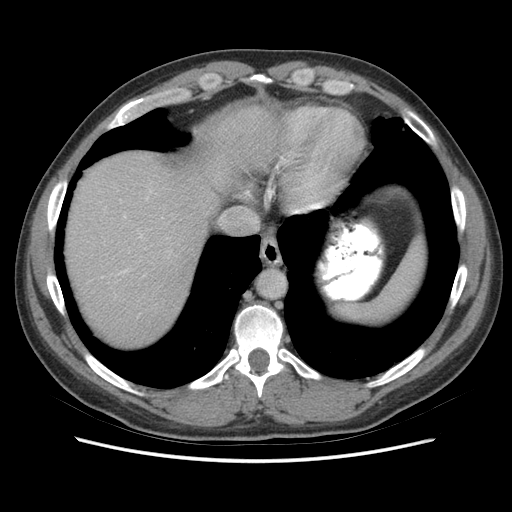
Contrast-enhanced abdominal CT (liver protocol), one axial slice. Soft-tissue window (W 400 / L 40 HU). 512 × 512 image matrix, field of view 360 × 360 mm. From the clinical record (not read from this slice): diagnosis: hepatocellular carcinoma (patient treated with transarterial chemoembolisation; whether this scan precedes or follows treatment is not stated here); TNM stage (as recorded): Stage-IIIA; Child-Pugh class: A; tumour size: 6.6 cm.
Outlined on this slice (semi-automatically segmented with operator editing):
- abdominal aorta: bounding box (x1, y1, x2, y2) in pixels: (258, 271, 286, 299)
- liver parenchyma outside the tumour (the mass and vessels are separate outlines, so this box may not span the whole liver): (66, 112, 248, 346)
- liver vessels: (124, 235, 142, 273)